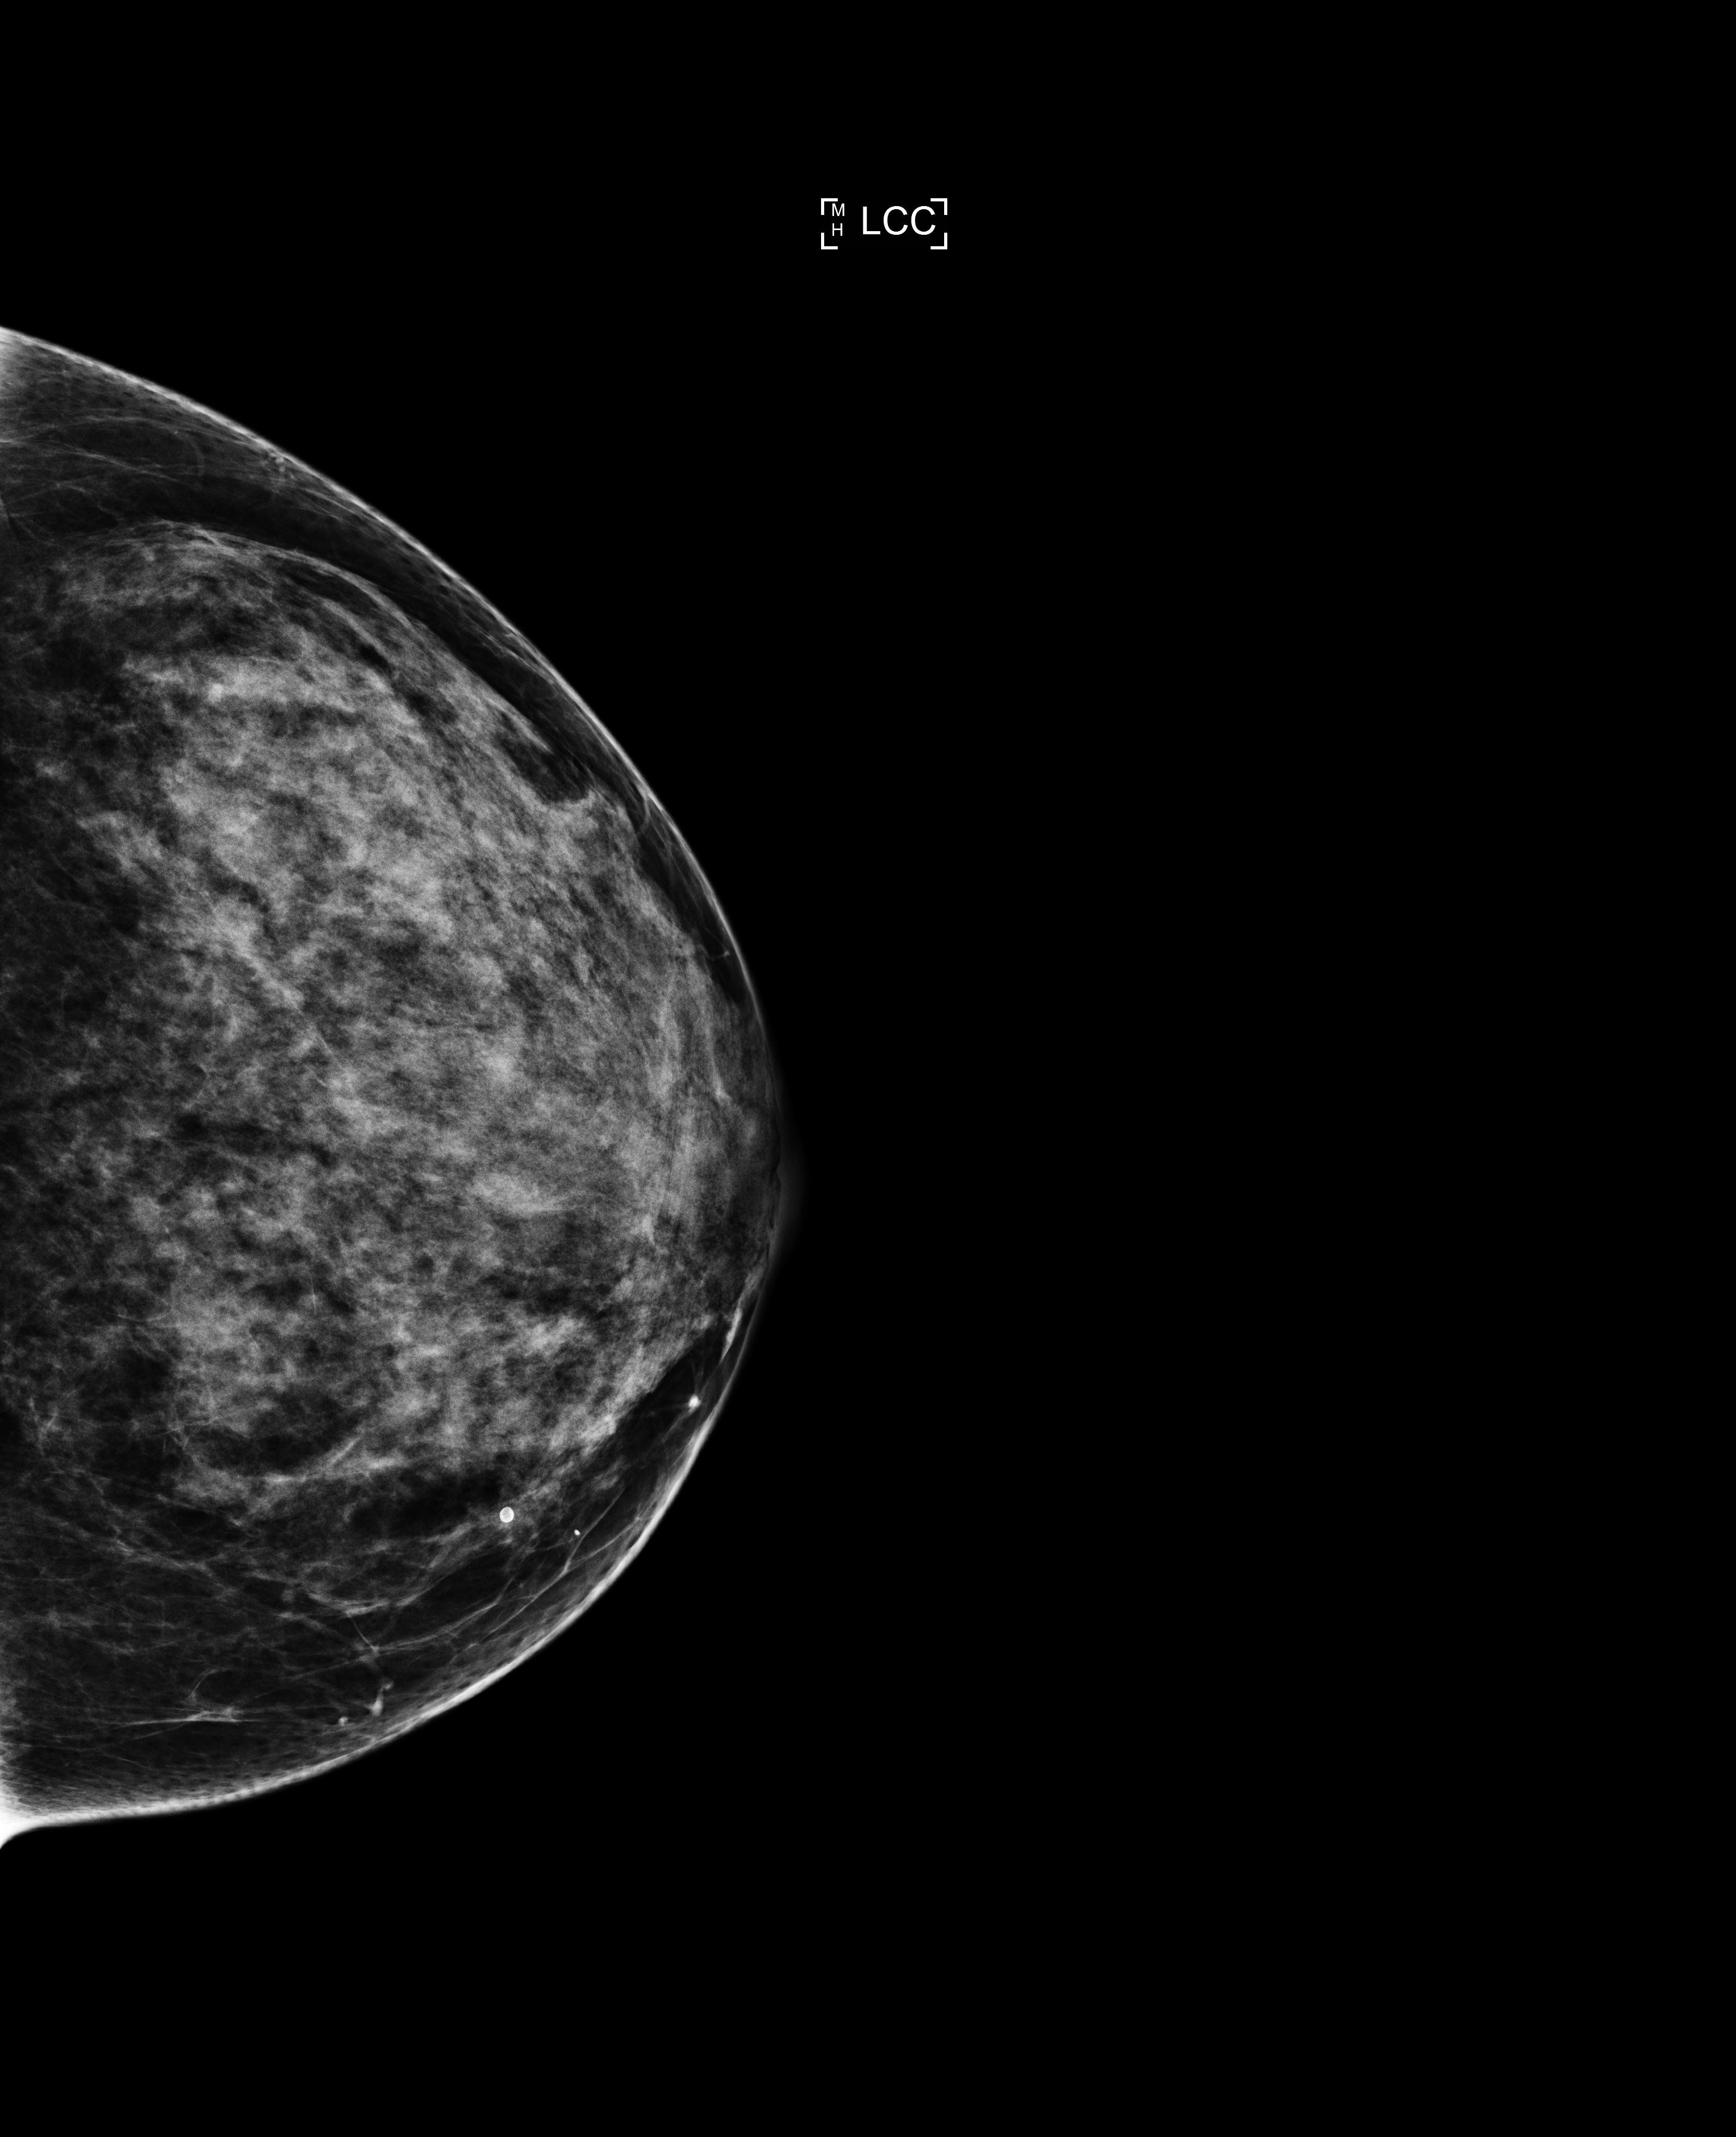
Digital mammogram (FFDM), left breast, CC view, annual screening mammography examination. Female patient, age 41 years.
- breast density at the screening exam (both breasts): extremely dense (BI-RADS density category d)
- final BI-RADS category for the screening round (tomosynthesis exam, both breasts): category 1
- recall: no recall after this screen